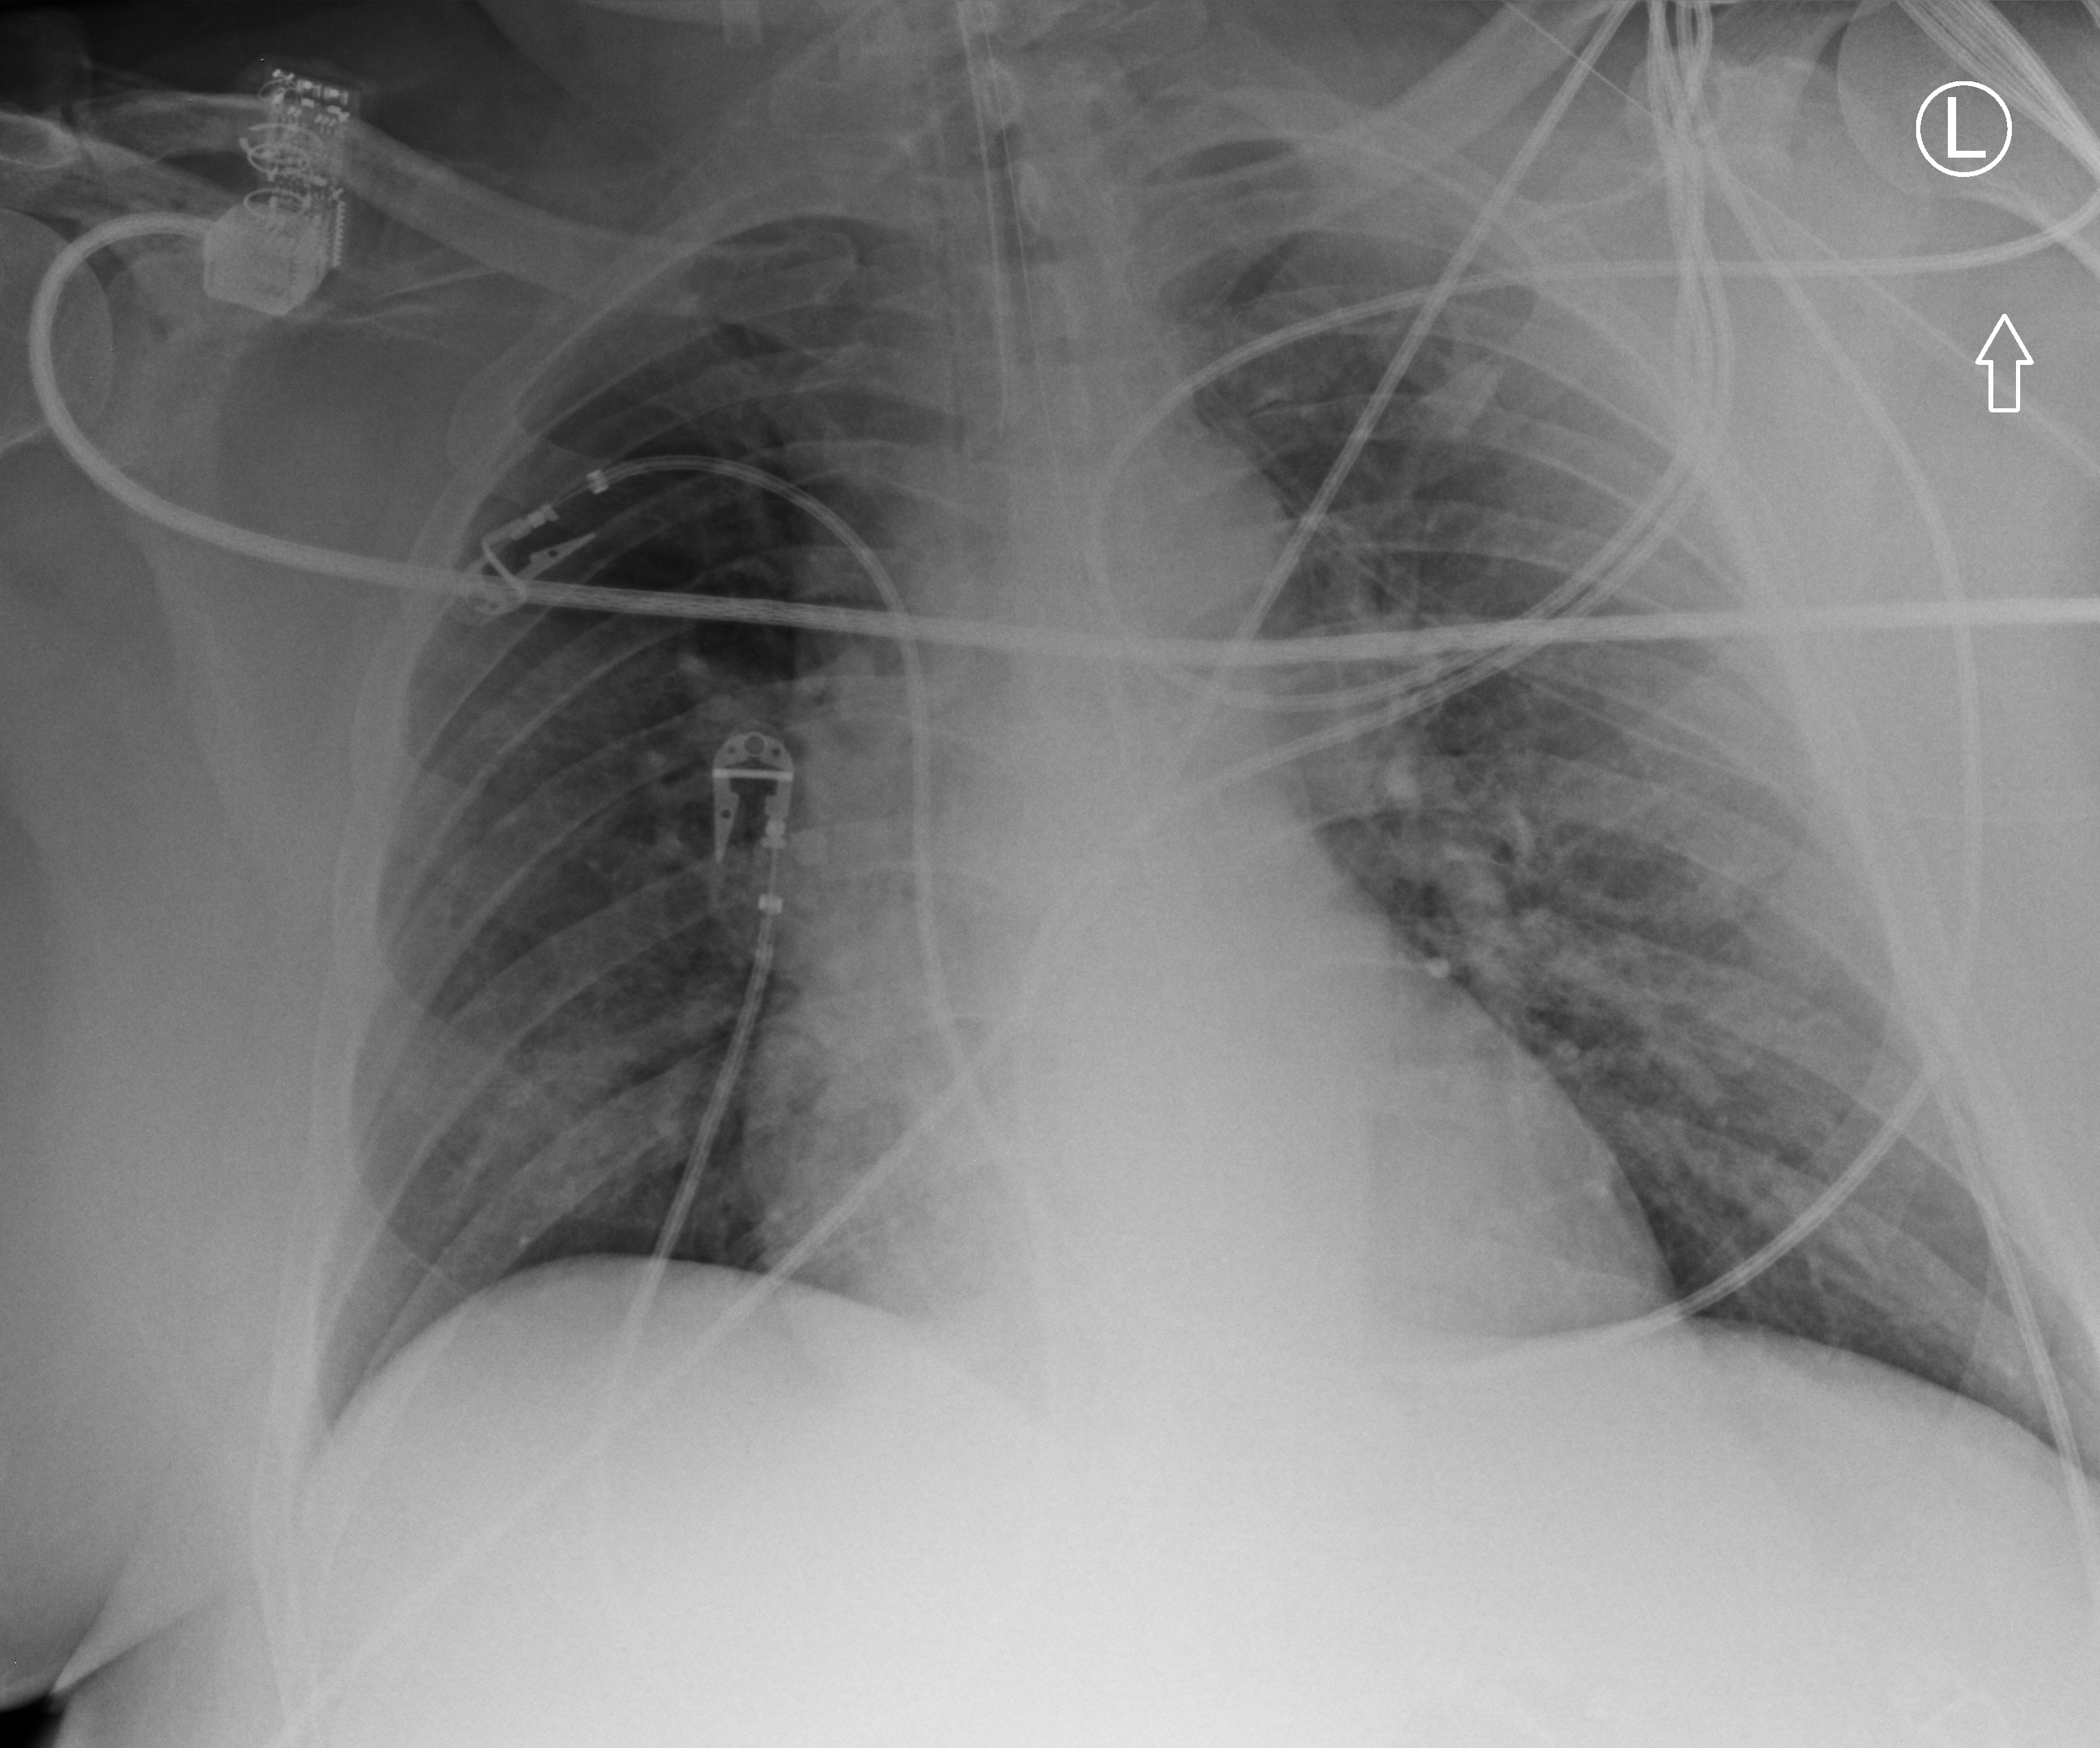
Chest X-ray (portable), anteroposterior (AP) projection. Male patient hospitalised with COVID-19, age 60–74 years.
Admission-level facts for this patient (not findings on this image; timing relative to this image not recorded): length of hospital stay: 17 days.